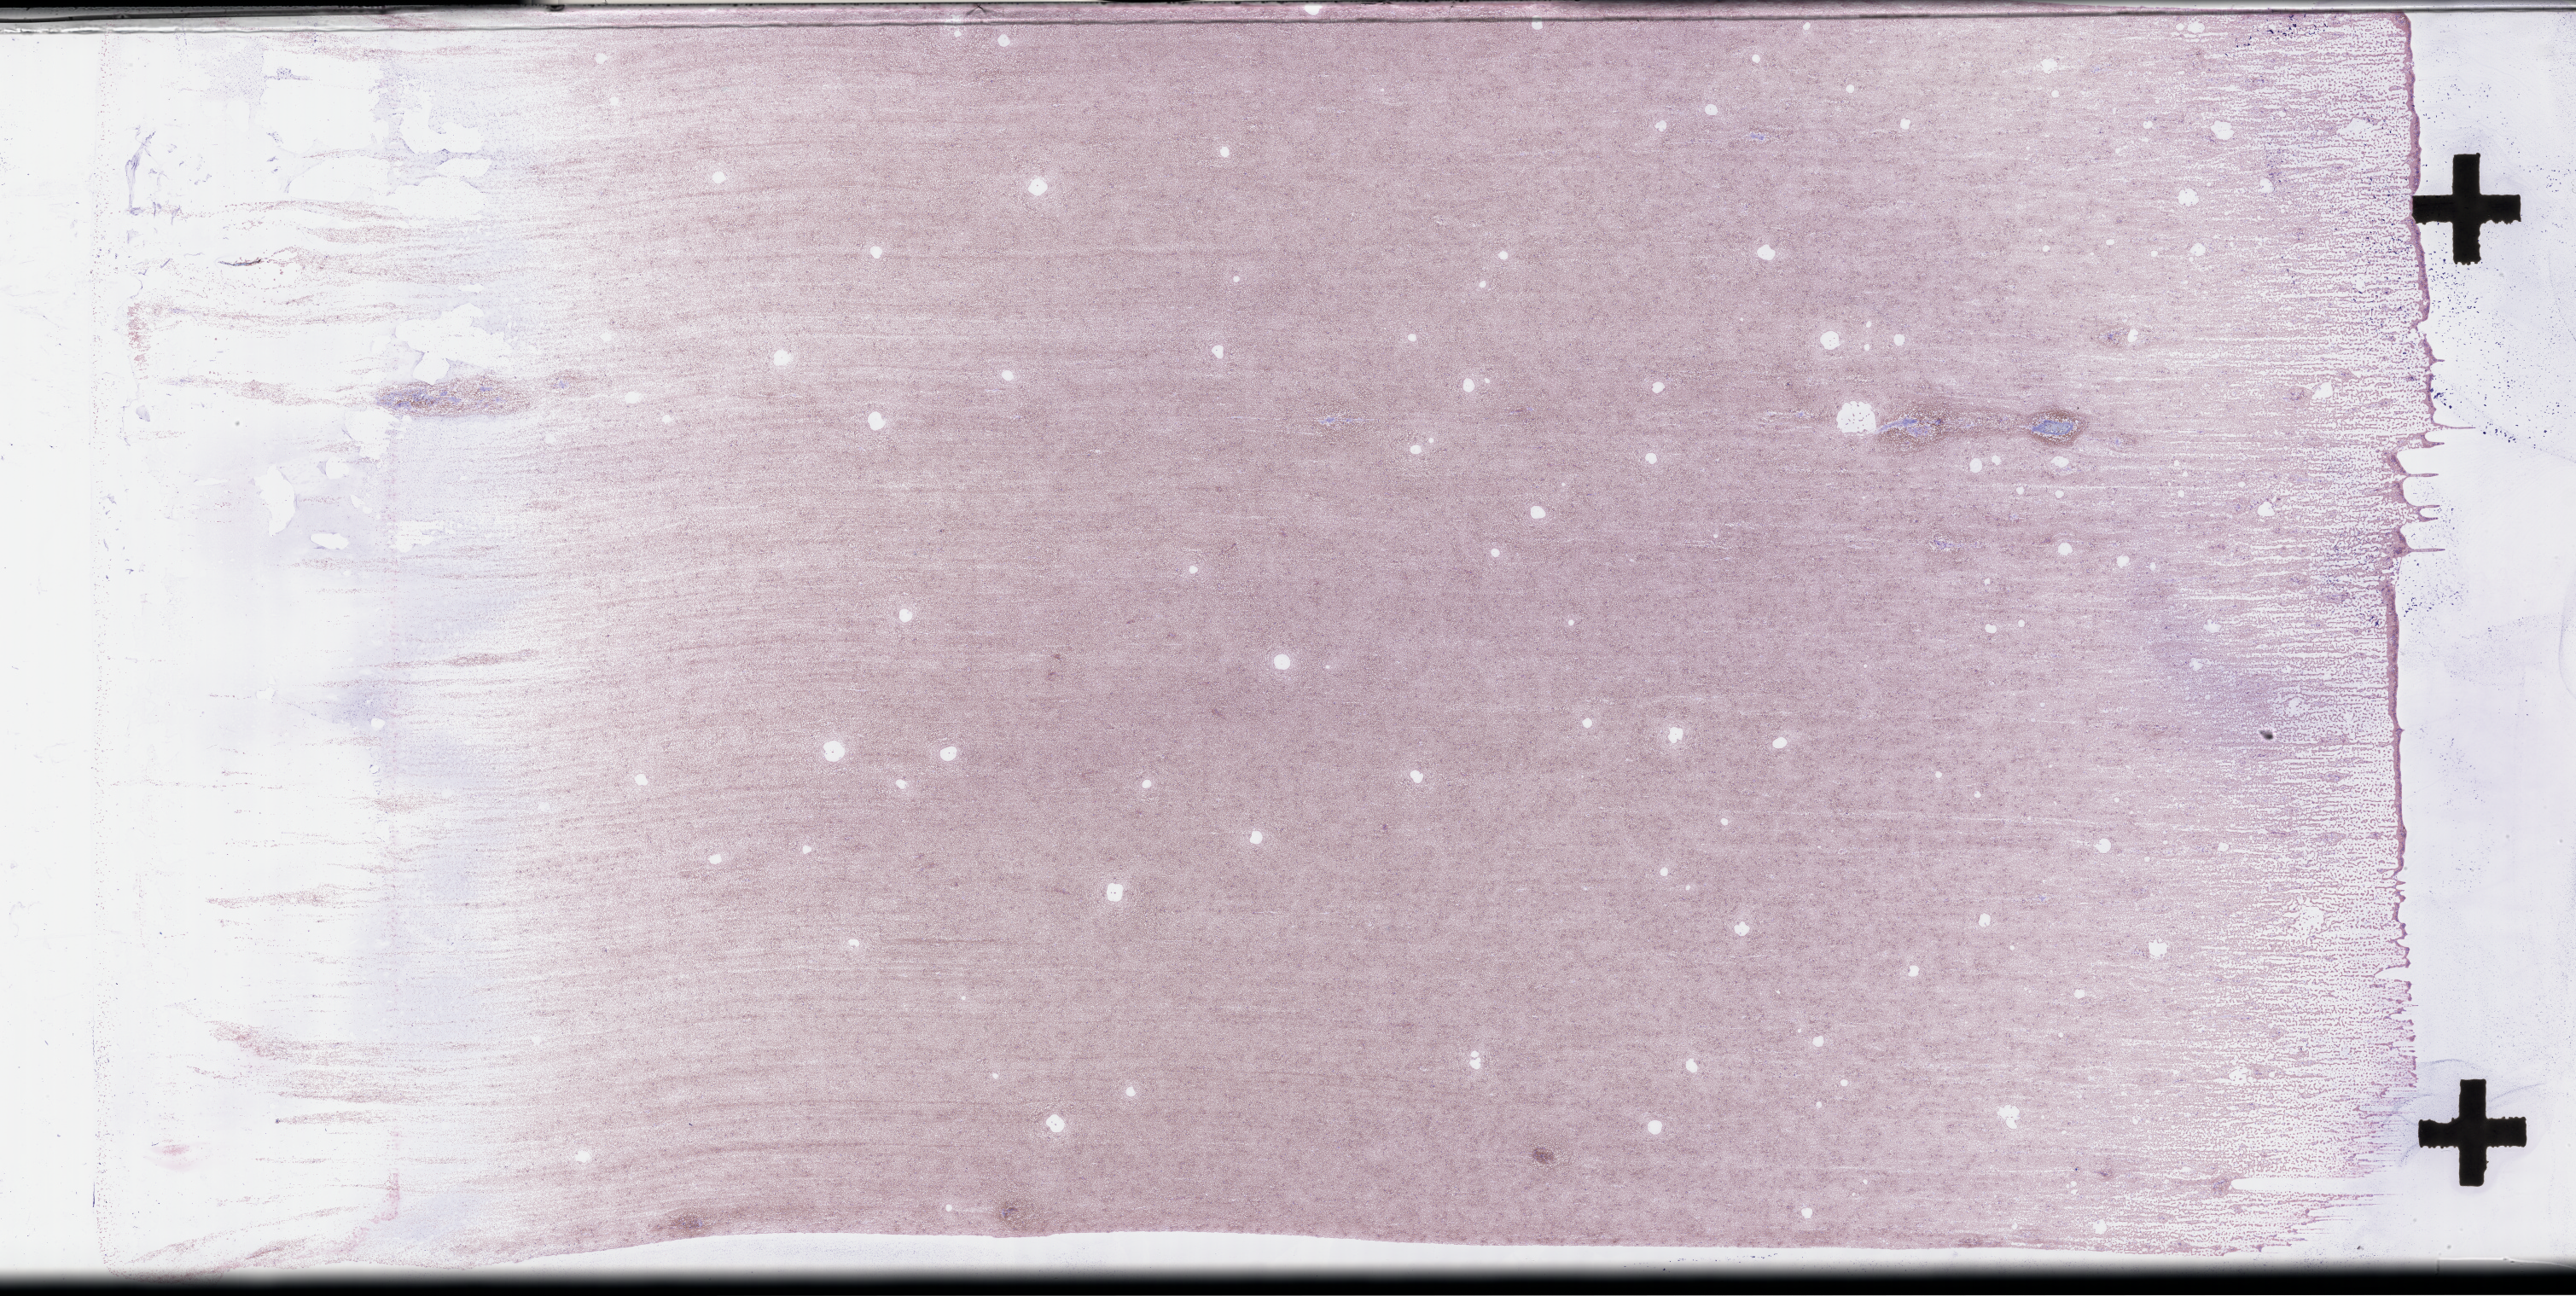
Wright–Giemsa-stained bone marrow smear, whole-slide image, whole scanned area (about 48.8 x 24.5 mm) shown as a low-resolution overview; collected on treatment. Patient sex: female.
• patient diagnosis: Acute Myeloid Leukemia Not Otherwise Specified